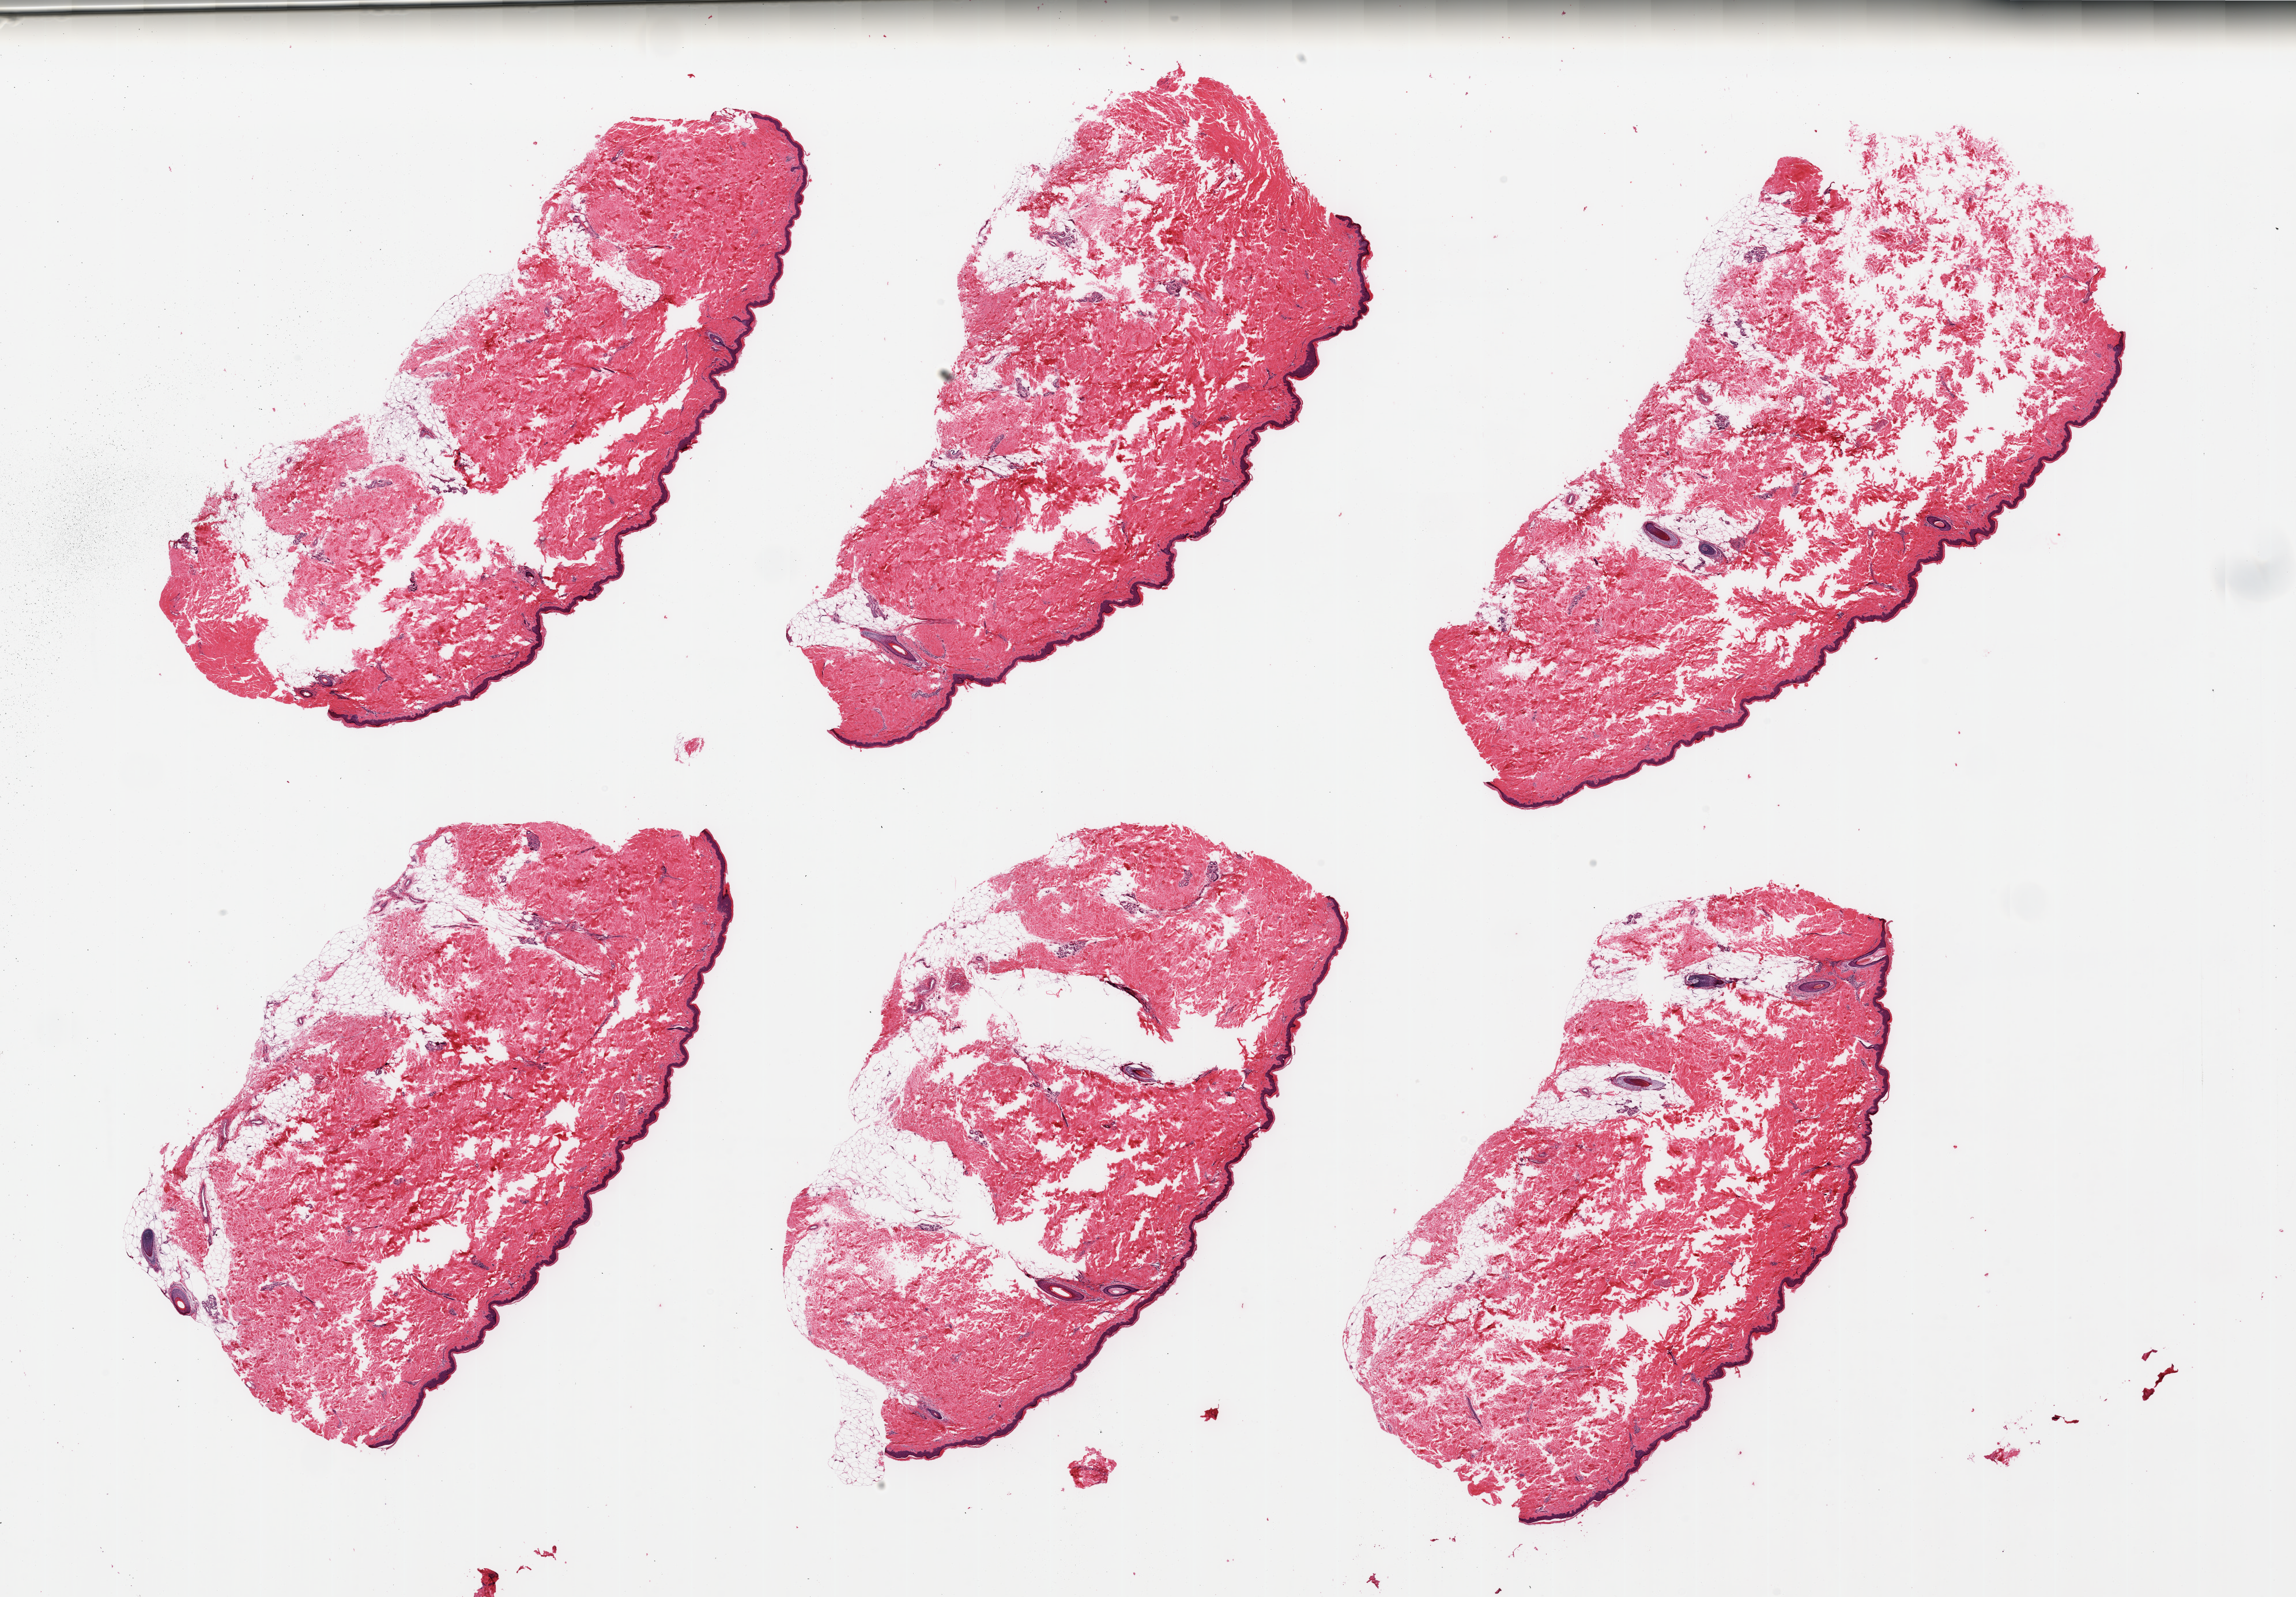
Digitized H&E-stained section, brightfield — low-resolution overview of the scanned area, about 31.5 x 21.9 mm. PAXgene-fixed, paraffin-embedded tissue. Target tissue: skin of lower leg. Donor tissue sample. Female donor.
Reviewer comment on this tissue sample: 6 pieces; several empty spaces; 10 to 20% internal/external fat; ~50.5 micron thick epidermis.